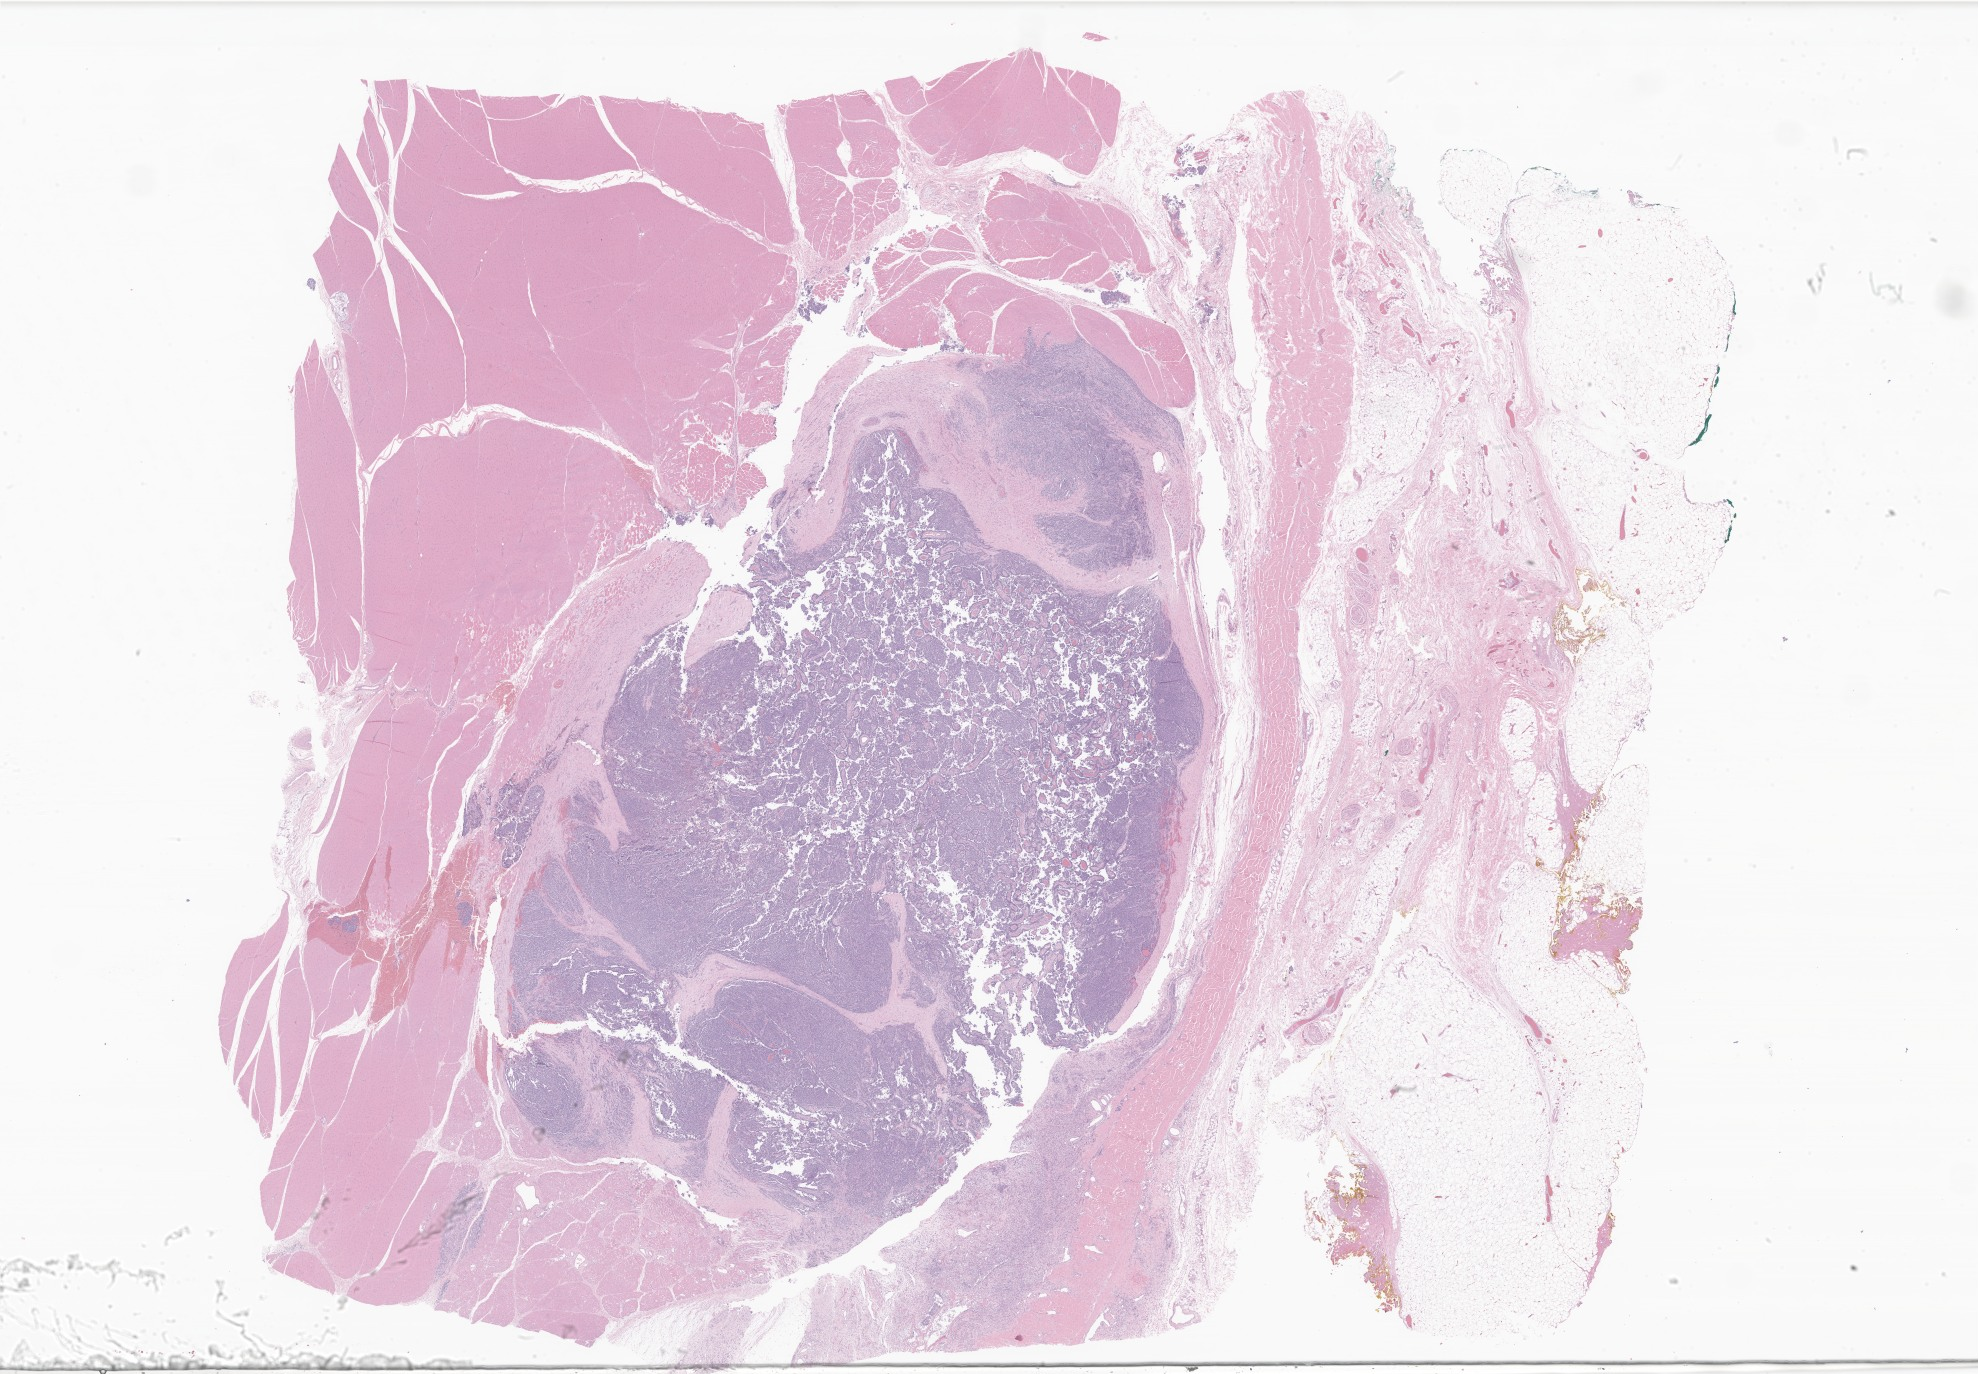
Digitized haematoxylin and eosin-stained section of tumor tissue from the lower limb, whole scanned area (about 33.4 x 23.2 mm) shown as a low-resolution overview; formalin-fixed, paraffin-embedded (FFPE) tissue. Female patient, age 56 months (4 years 8 months).
Recorded diagnosis: Alveolar rhabdomyosarcoma.